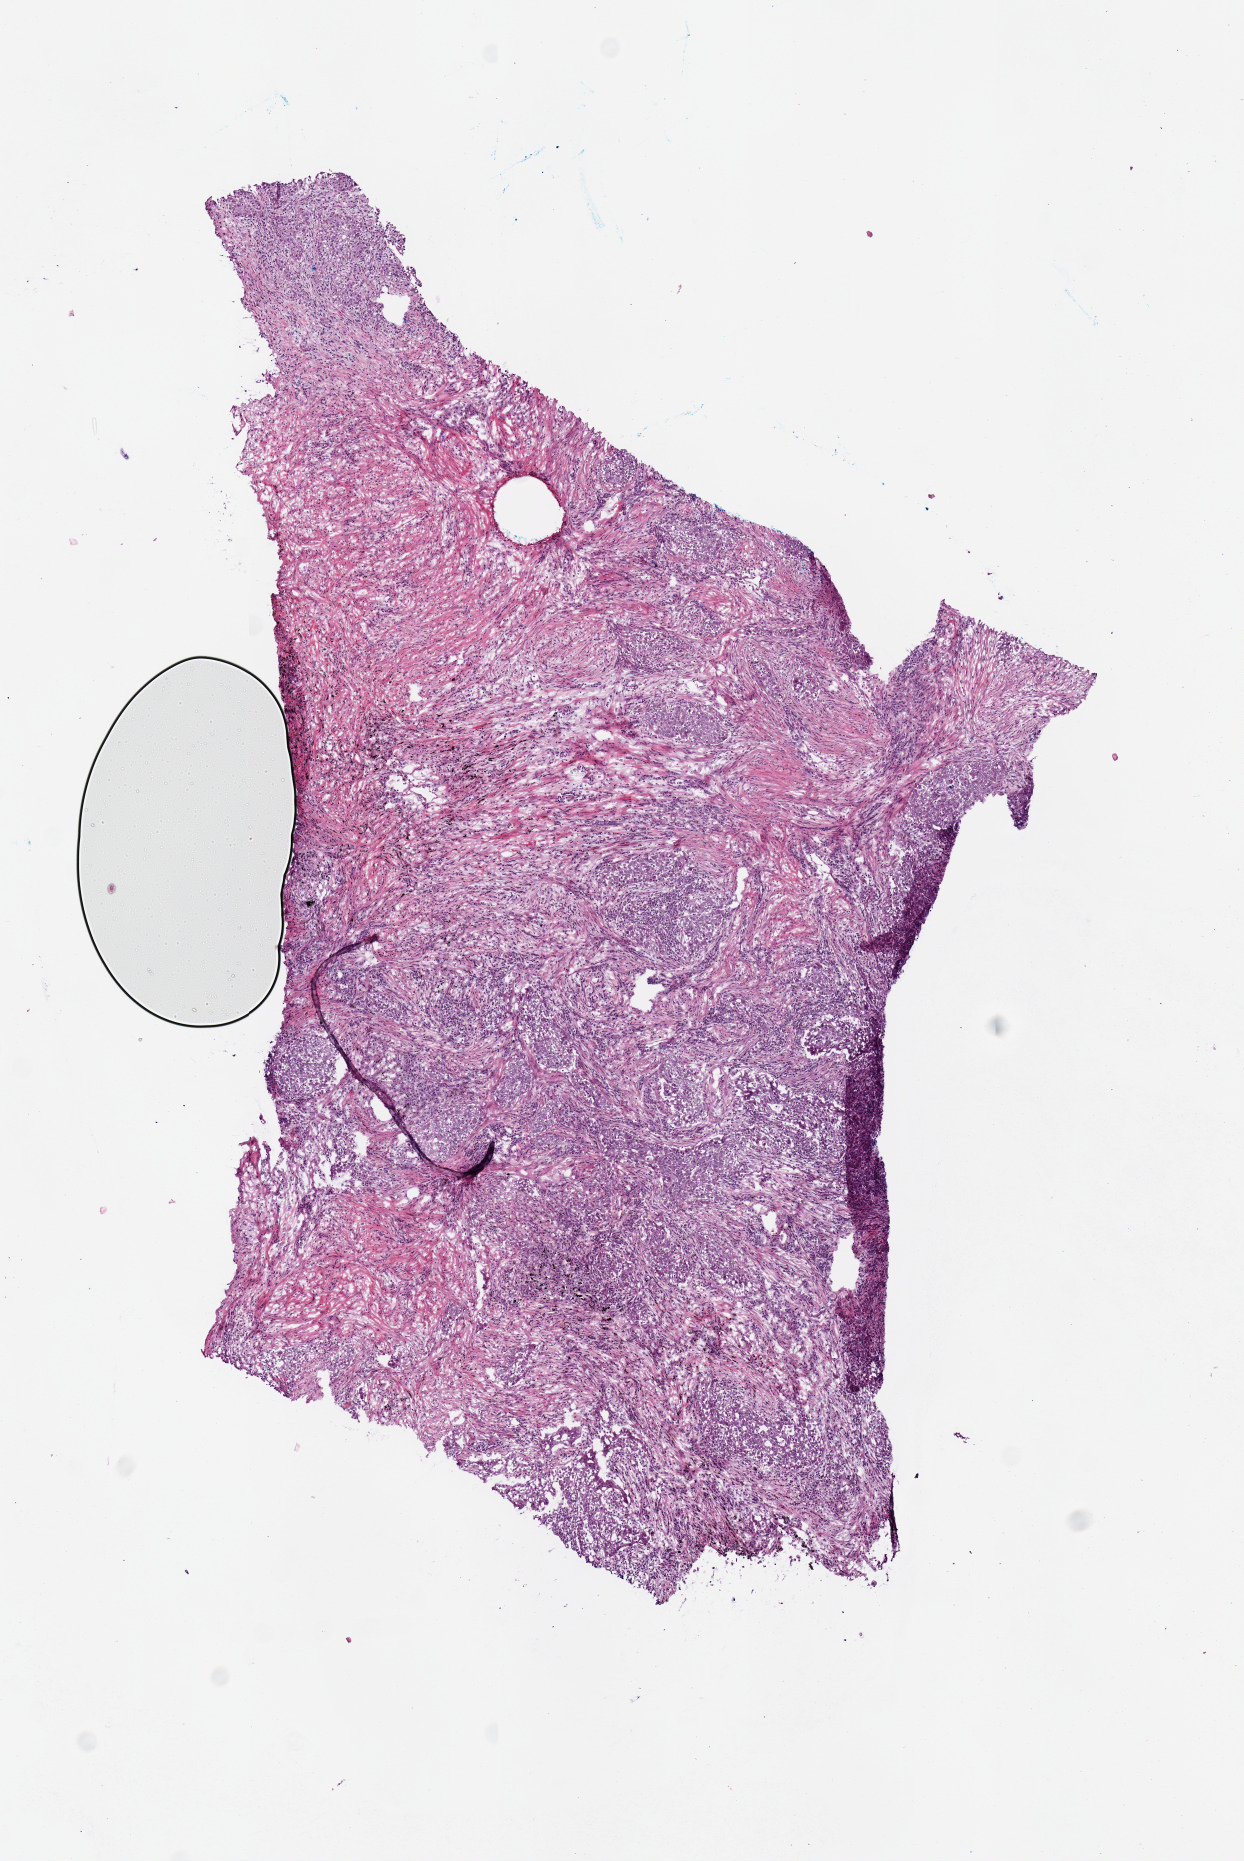
Whole-slide histology image, Hematoxylin and eosin (H&E) stained, a low-resolution overview of the entire scanned area, about 4.9 x 7.4 mm, frozen section from the bottom of the tissue portion, lung, primary tumour sample. Patient: female, age at initial diagnosis 59 years.
Laterality: left. AJCC pathologic stage: IIB (6th edition). Diagnosis: Adenocarcinoma, NOS (upper lobe, lung).